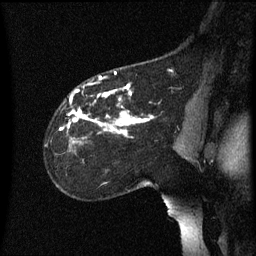
Breast MRI (dynamic contrast-enhanced), one sagittal slice. Position 41 of 60 along the scan axis. Dynamic contrast-enhanced series, image 2 of 3 at this slice position (ordered by acquisition). 1.5 T. TE 4.2 ms, TR 8.4 ms. 2.2 mm slice thickness. 256 × 256 image matrix, field of view 200 × 200 mm. Female patient, age 35 years. From the clinical record (not read from this slice): setting: breast cancer imaged before/during neoadjuvant chemotherapy; receptor status: HER2-positive.
Outlined on this slice (semi-automatically segmented with operator editing):
- analysis volume of interest (the breast-tissue region the enhancement analysis was run in; not a lesion): bounding box (x1, y1, x2, y2) in pixels: (45, 72, 178, 173)
- tumour enhancement mask (voxels above the 70 % enhancement threshold inside the analysis volume of interest): (60, 72, 154, 139)